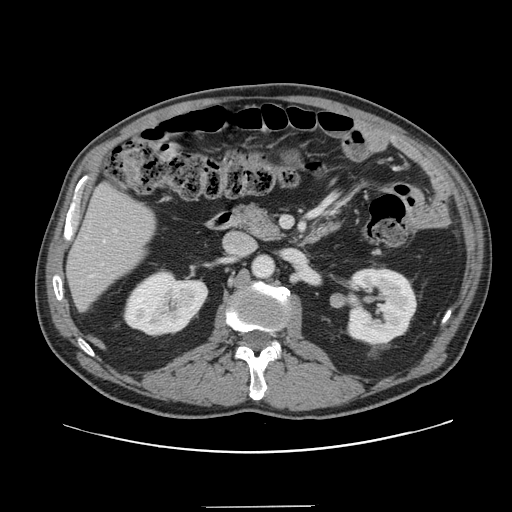
Contrast-enhanced abdominal CT, one axial slice. Slice 63 of 139 in the series (ordered by position). Intravenous contrast given. Soft-tissue window (W 400 / L 40 HU). 2.5 mm slice thickness. 512 × 512 image matrix, field of view 397 × 397 mm. Male patient, age 64 years. Case-level facts recorded for this patient, not image findings: diagnosis: colorectal cancer liver metastases, imaged before liver resection; multiple liver metastases: yes.
Annotated regions visible in this slice (expert manual segmentation):
- liver: bounding box <68,187,156,309> (left, top, right, bottom; pixels)
- planned liver remnant (the part of the liver to remain after resection): <68,187,156,309>
- portal vein (with intrahepatic branches): <114,230,117,232>